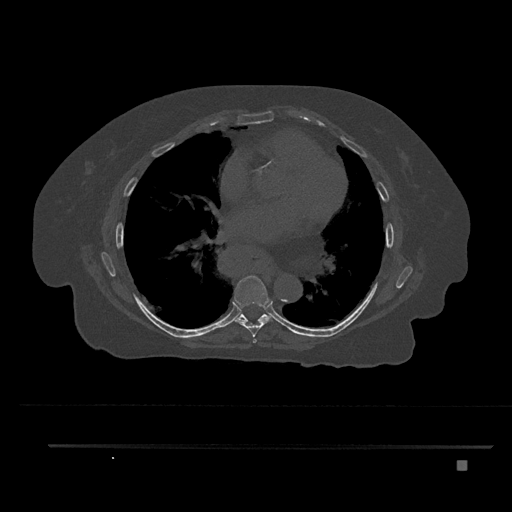
CT including the spine, one axial slice; position 469 of 797 along the scan axis; reconstruction kernel Br40s/3; 120 kVp; bone window (W 1800 / L 400 HU); 0.5 mm slice thickness; 512 × 512 image matrix. Patient: female, 76 years. Case-level facts recorded for this patient, not image findings: primary cancer: lung; vertebrae with lytic lesions (as recorded): T11, L3.
Outlined on this slice (semi-automatically segmented with operator editing):
- T6 vertebra: bounding box [x1, y1, x2, y2] px = [253, 339, 257, 343]
- T7 vertebra: [234, 275, 273, 337]
- T8 vertebra: [237, 313, 271, 322]